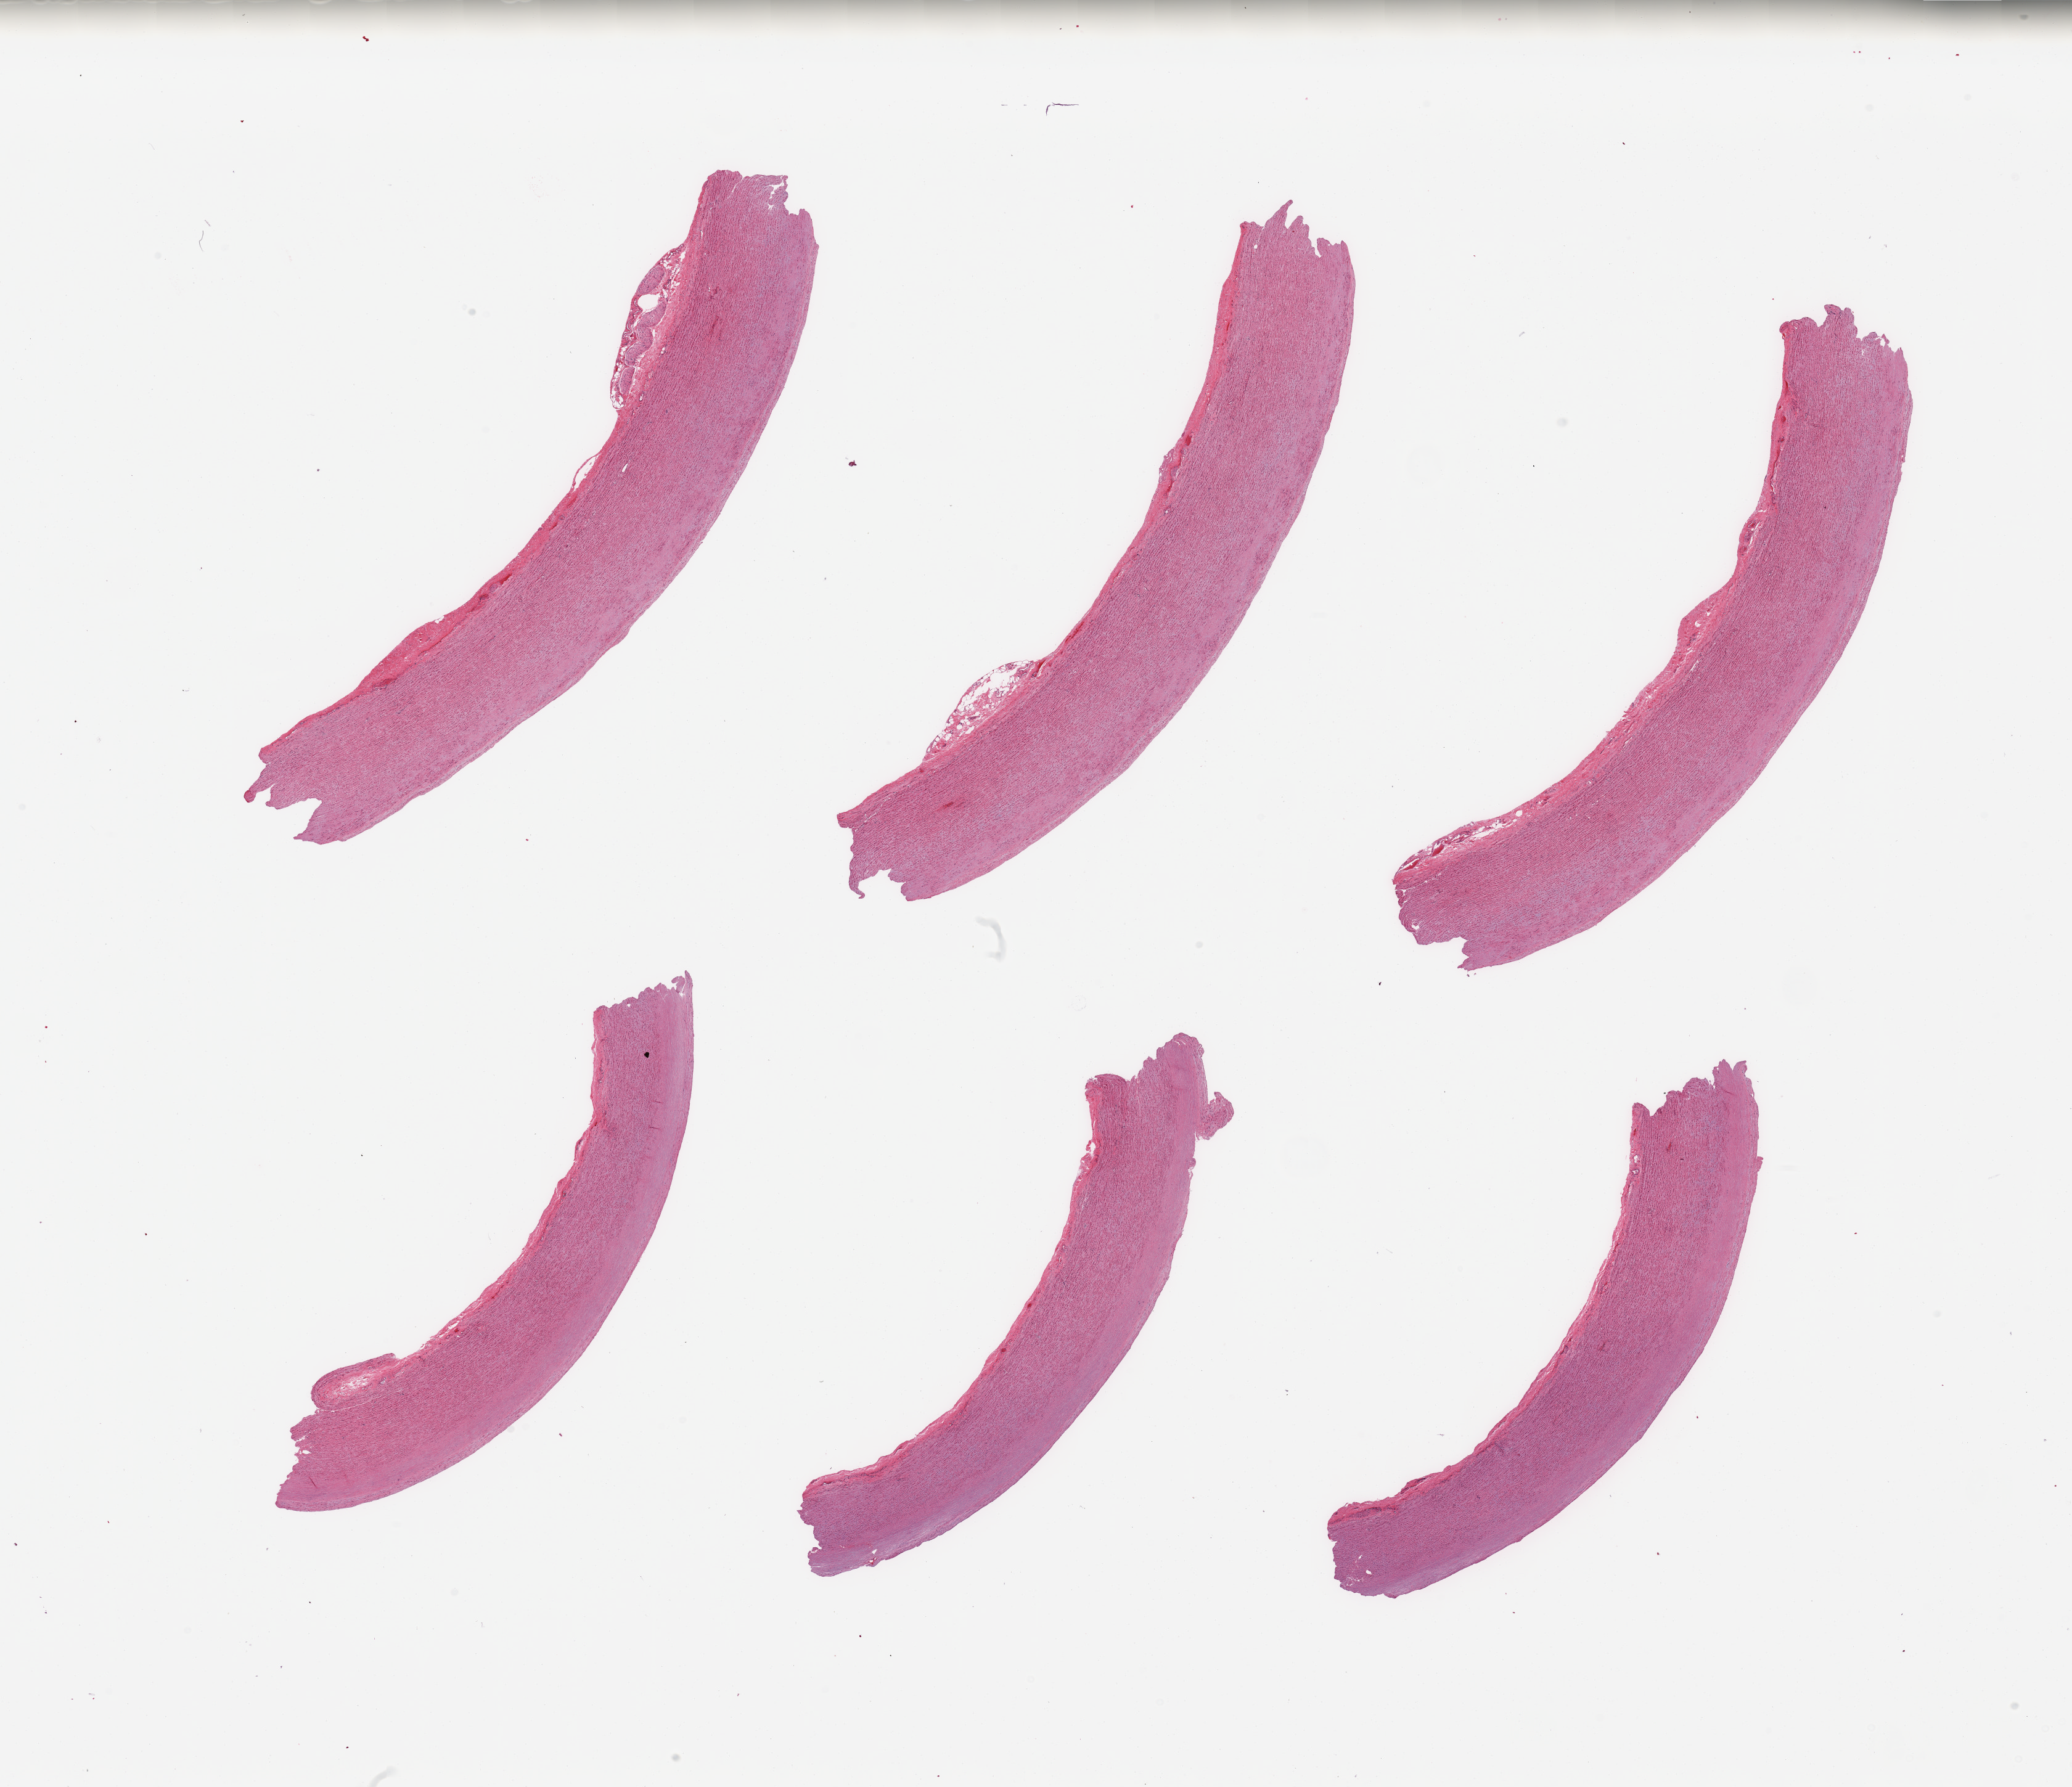
Haematoxylin and eosin whole-slide image, brightfield, whole scanned area (about 26.6 x 22.9 mm, slide scanned at 20x) shown as a low-resolution overview, PAXgene-fixed, paraffin-embedded tissue, sampled site (target tissue): aorta, donor tissue sample. Female donor.
Review note (as recorded): 6 pieces; minimal plaque; well trimmed.